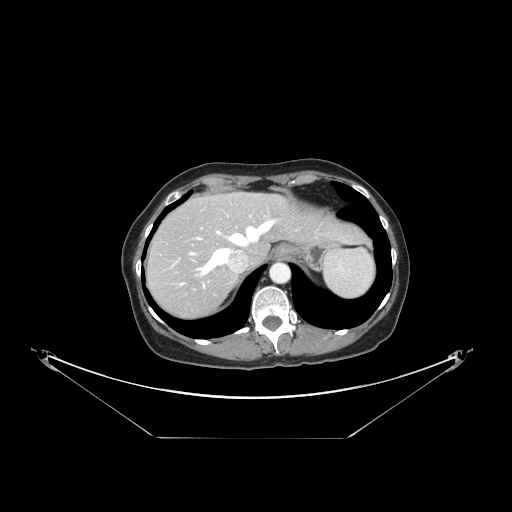
Contrast-enhanced abdominal CT, one axial slice; position 122 of 148 along the scan axis; reconstruction kernel STANDARD; intravenous contrast given; soft-tissue window (W 400 / L 40 HU); 2.5 mm slice thickness; 512 × 512 image matrix, field of view 500 × 500 mm. Female patient, age 73 years. From the clinical record (not read from this slice): diagnosis: colorectal cancer liver metastases, imaged before liver resection; multiple liver metastases: no; largest metastasis: 1 cm; disease in both lobes: no.
Annotated regions visible in this slice (outlined manually by an expert reader):
- hepatic veins: bounding box [x1, y1, x2, y2] px = [192, 219, 276, 275]
- liver: [148, 194, 363, 316]
- planned liver remnant (the part of the liver to remain after resection): [174, 194, 363, 263]